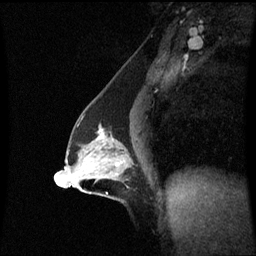
Breast MRI (dynamic contrast-enhanced), one sagittal slice; slice 36 of 60 in the series (ordered by position); dynamic contrast-enhanced series, image 2 of 3 at this slice position (ordered by acquisition); 1.5 T; TE 4.2 ms, TR 8.9 ms; 2.2 mm slice thickness; 256 × 256 image matrix, field of view 210 × 210 mm. Female patient, age 47 years. From the clinical record (not read from this slice): setting: breast cancer imaged before/during neoadjuvant chemotherapy; receptor status: HR-positive, HER2-negative.
Structures marked on this image (semi-automatic segmentation, software-assisted and operator-edited):
- analysis volume of interest (the breast-tissue region the enhancement analysis was run in; not a lesion): box from (x=64, y=122) to (x=134, y=196) px
- tumour enhancement mask (voxels above the 70 % enhancement threshold inside the analysis volume of interest): (x=97, y=135)–(x=120, y=167)